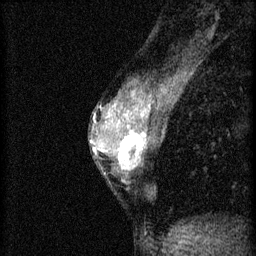
Breast MRI (dynamic contrast-enhanced), one sagittal slice; slice 28 of 46 in the series (ordered by position); 3 images stored at this slice position (order not interpretable as contrast timing); 1.5 T; TE 4.2 ms, TR 8.2 ms; 256 × 256 image matrix, field of view 180 × 180 mm. Female patient, age 44 years.
Outlined on this slice (semi-automatic segmentation, software-assisted and operator-edited):
- analysis volume of interest (the breast-tissue region the enhancement analysis was run in; not a lesion): bounding box [x1, y1, x2, y2] px = [110, 128, 156, 177]
- tumour enhancement mask (voxels above the 70 % enhancement threshold inside the analysis volume of interest): [118, 128, 149, 171]